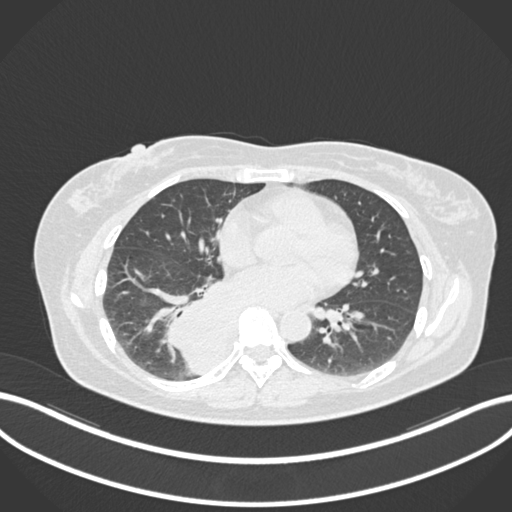
Chest CT, one axial slice. Position 573 of 677 along the scan axis. Reconstruction kernel B30f. Lung window (W 1500 / L -600 HU). 1 mm slice thickness. 512 × 512 image matrix, field of view 400 × 400 mm. Patient: female, 54 years. Case-level facts recorded for this patient, not image findings: clinical TNM (as recorded): T4 N0 M0.
Structures marked on this image (rectangle marked by the reading radiologist):
- lung tumour (recorded histology: adenocarcinoma): bounding box (x1, y1, x2, y2) in pixels: (162, 269, 244, 375)